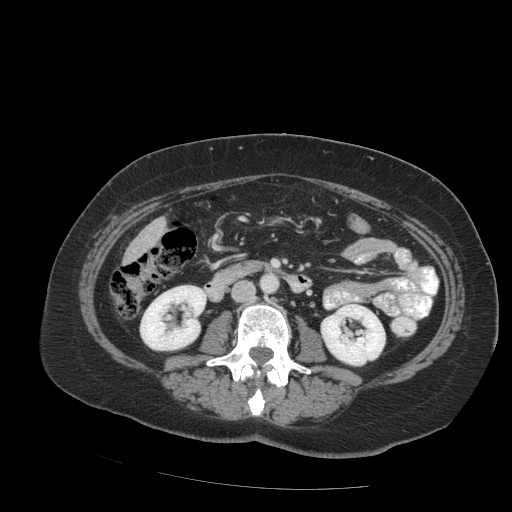
Contrast-enhanced abdominal CT (liver protocol), one axial slice. Slice 21 of 99 in the series (ordered by position). 140 kVp. Soft-tissue window (W 400 / L 40 HU). 2.5 mm slice thickness. 512 × 512 image matrix, field of view 400 × 400 mm. From the clinical record (not read from this slice): diagnosis: hepatocellular carcinoma (patient treated with transarterial chemoembolisation; whether this scan precedes or follows treatment is not stated here); TNM stage (as recorded): Stage-IVB.
Outlined on this slice (semi-automatic segmentation, software-assisted and operator-edited):
- liver parenchyma outside the tumour (the mass and vessels are separate outlines, so this box may not span the whole liver): bounding box <124,217,166,262> (left, top, right, bottom; pixels)